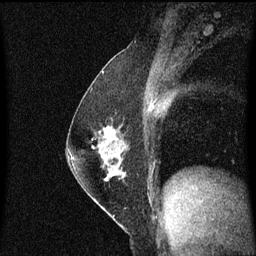
Breast MRI (dynamic contrast-enhanced), one sagittal slice; dynamic contrast-enhanced series, image 2 of 3 at this slice position (ordered by acquisition); 1.5 T; TE 4.2 ms, TR 8.4 ms; 256 × 256 image matrix, field of view 200 × 200 mm. Patient: female, 52 years. From the clinical record (not read from this slice): setting: breast cancer imaged before/during neoadjuvant chemotherapy; receptor status: HER2-positive.
Annotated regions visible in this slice (semi-automatically segmented with operator editing):
- analysis volume of interest (the breast-tissue region the enhancement analysis was run in; not a lesion): box from (x=71, y=118) to (x=131, y=187) px
- tumour enhancement mask (voxels above the 70 % enhancement threshold inside the analysis volume of interest): (x=104, y=126)–(x=117, y=181)